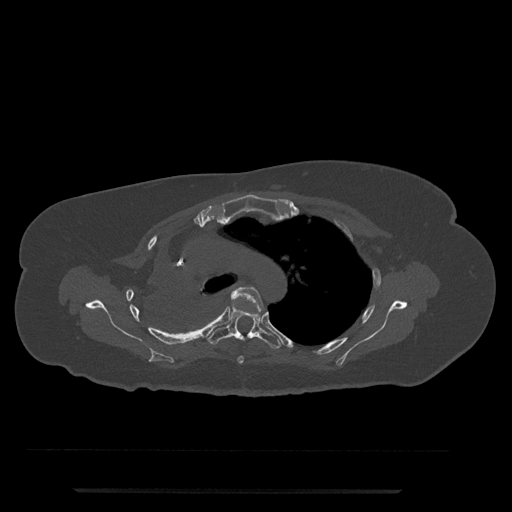
CT including the spine, one axial slice; slice 559 of 797 in the series (ordered by position); reconstruction kernel Br40s/3; 120 kVp; bone window (W 1800 / L 400 HU); 0.5 mm slice thickness; 512 × 512 image matrix, field of view 440 × 440 mm. Female patient, age 51 years. Case-level facts recorded for this patient, not image findings: primary cancer: neuro; vertebrae with lytic lesions (as recorded): T8.
Annotated regions visible in this slice (semi-automatic segmentation, software-assisted and operator-edited):
- T4 vertebra: bounding box (x1, y1, x2, y2) in pixels: (231, 287, 264, 364)
- T5 vertebra: (206, 305, 282, 349)